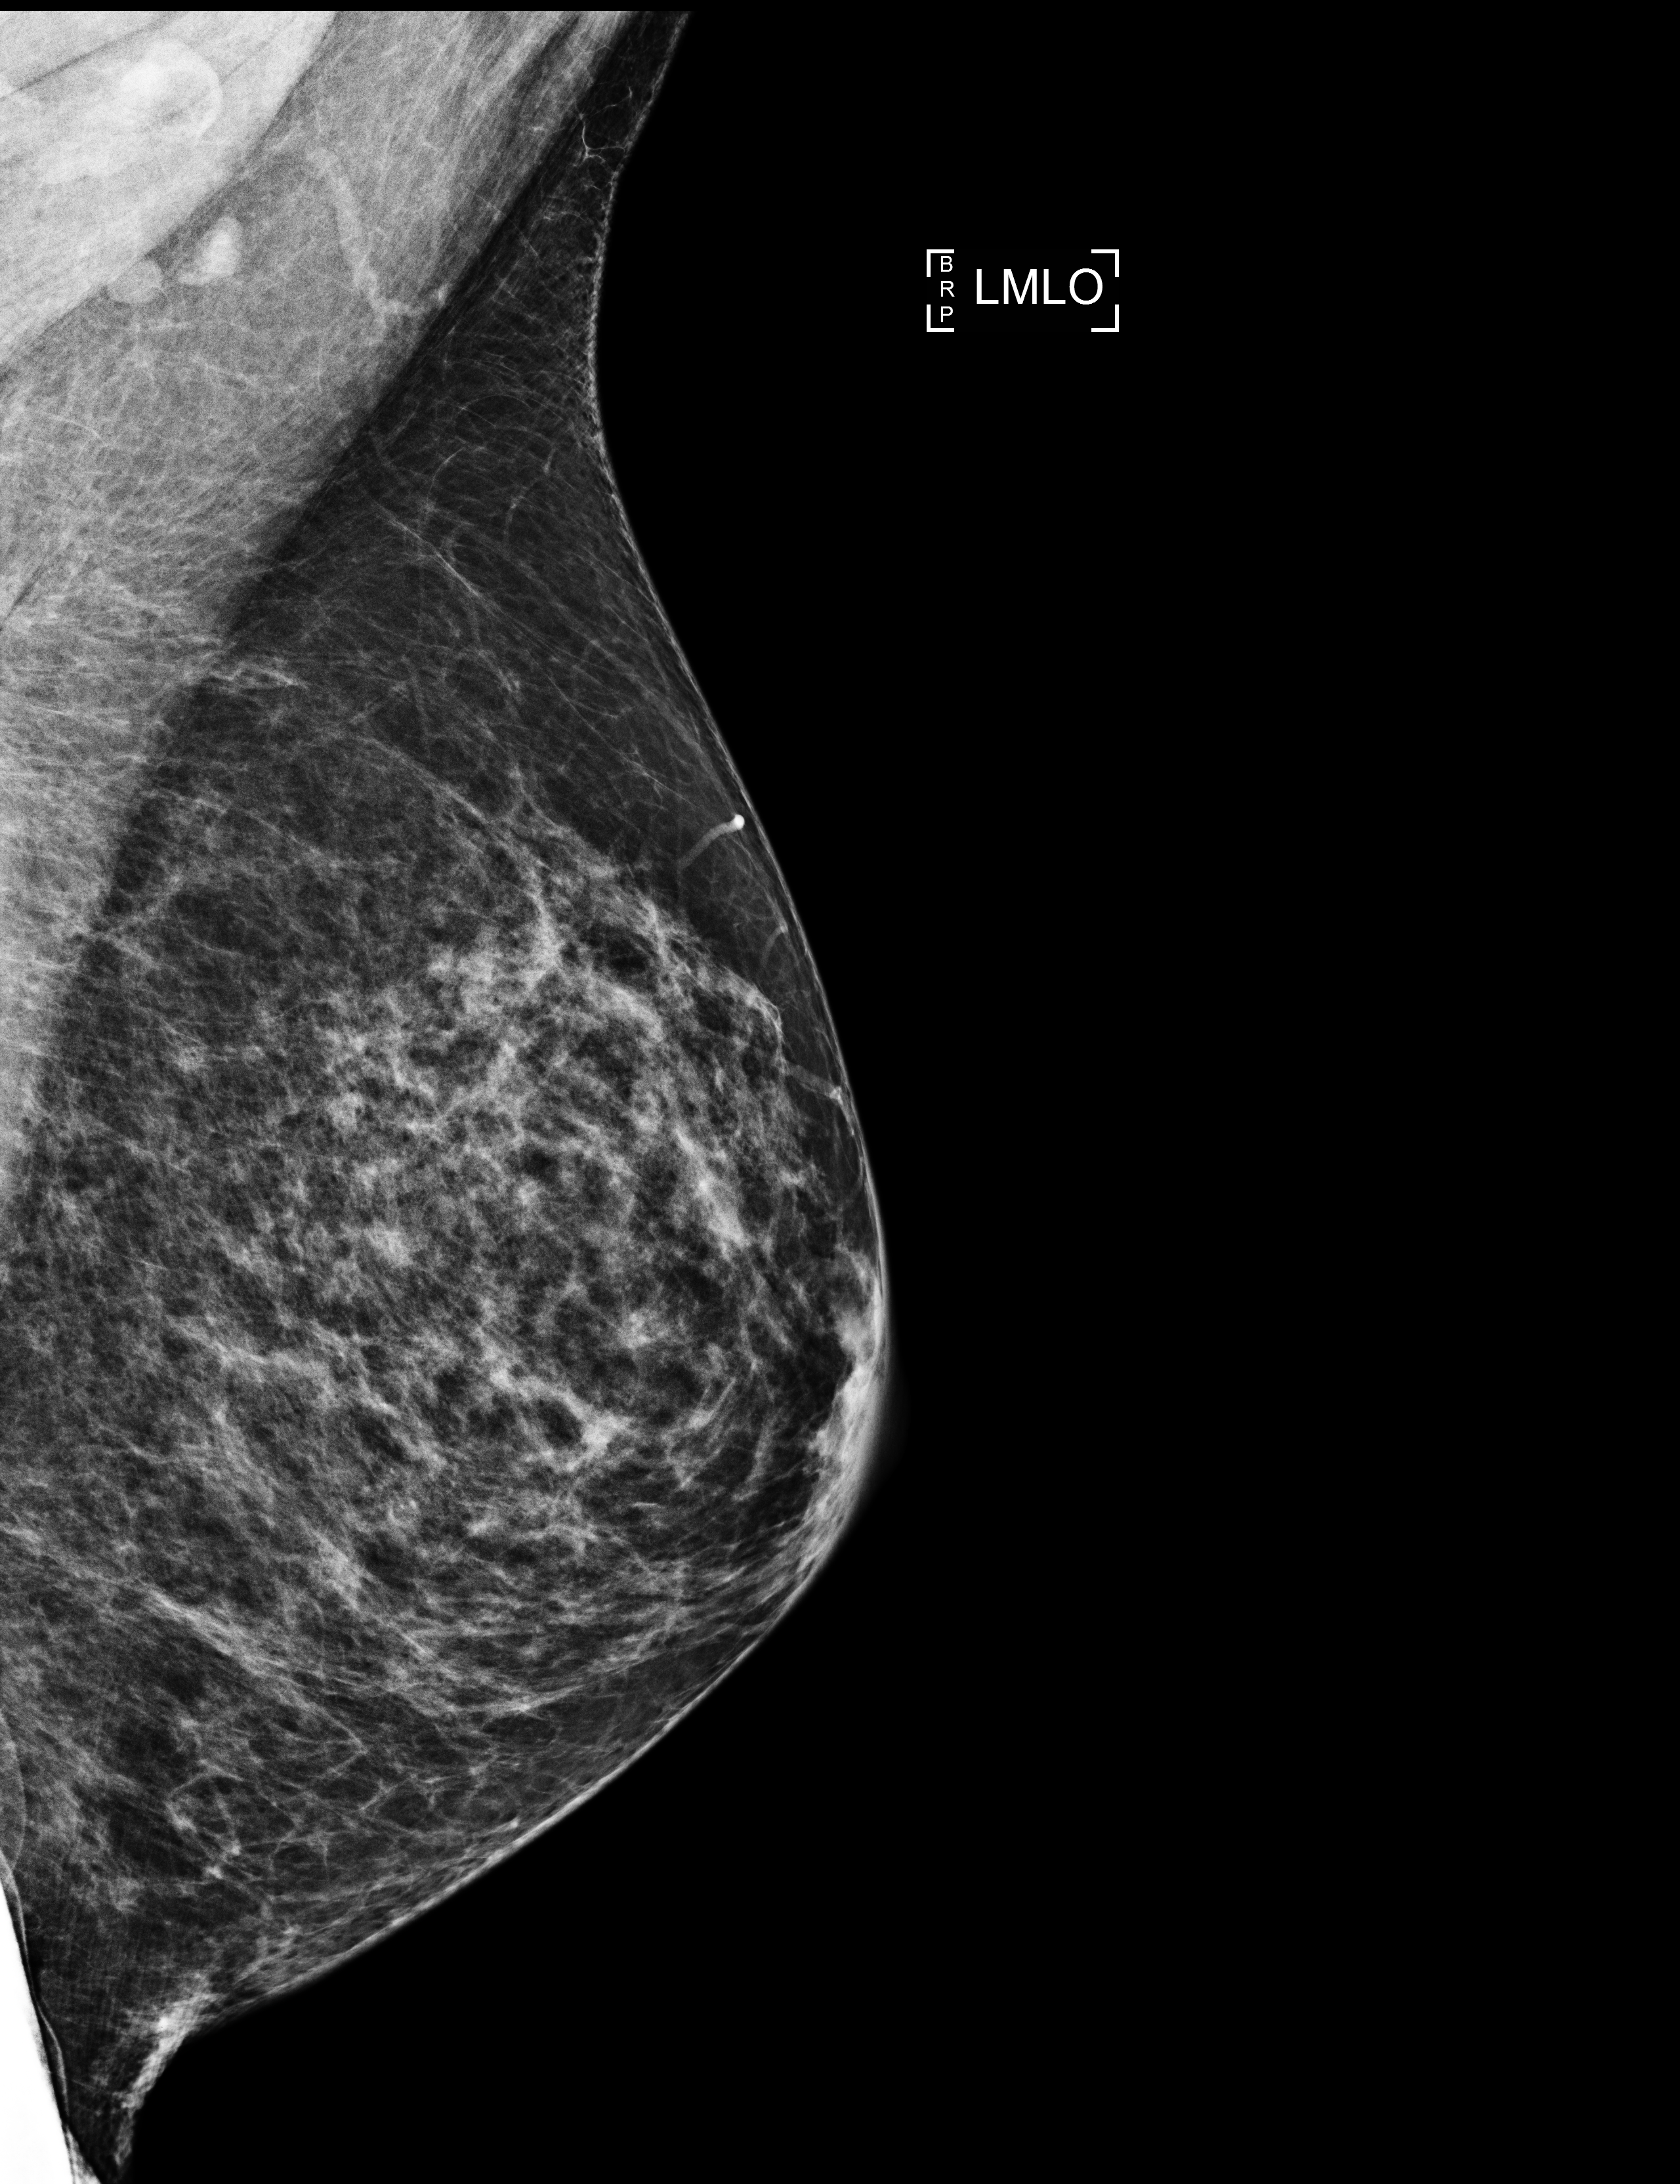
Annual screening mammography examination. Patient: female, 63 years.
Image type: full-field digital mammogram. Breast: left. Projection: medio-lateral oblique projection. BI-RADS breast density category at the screening exam (both breasts, scale 1–4): 3. Final BI-RADS assessment for this screening round (tomosynthesis exam, both breasts): category 2. Recall: no recall after this screen.